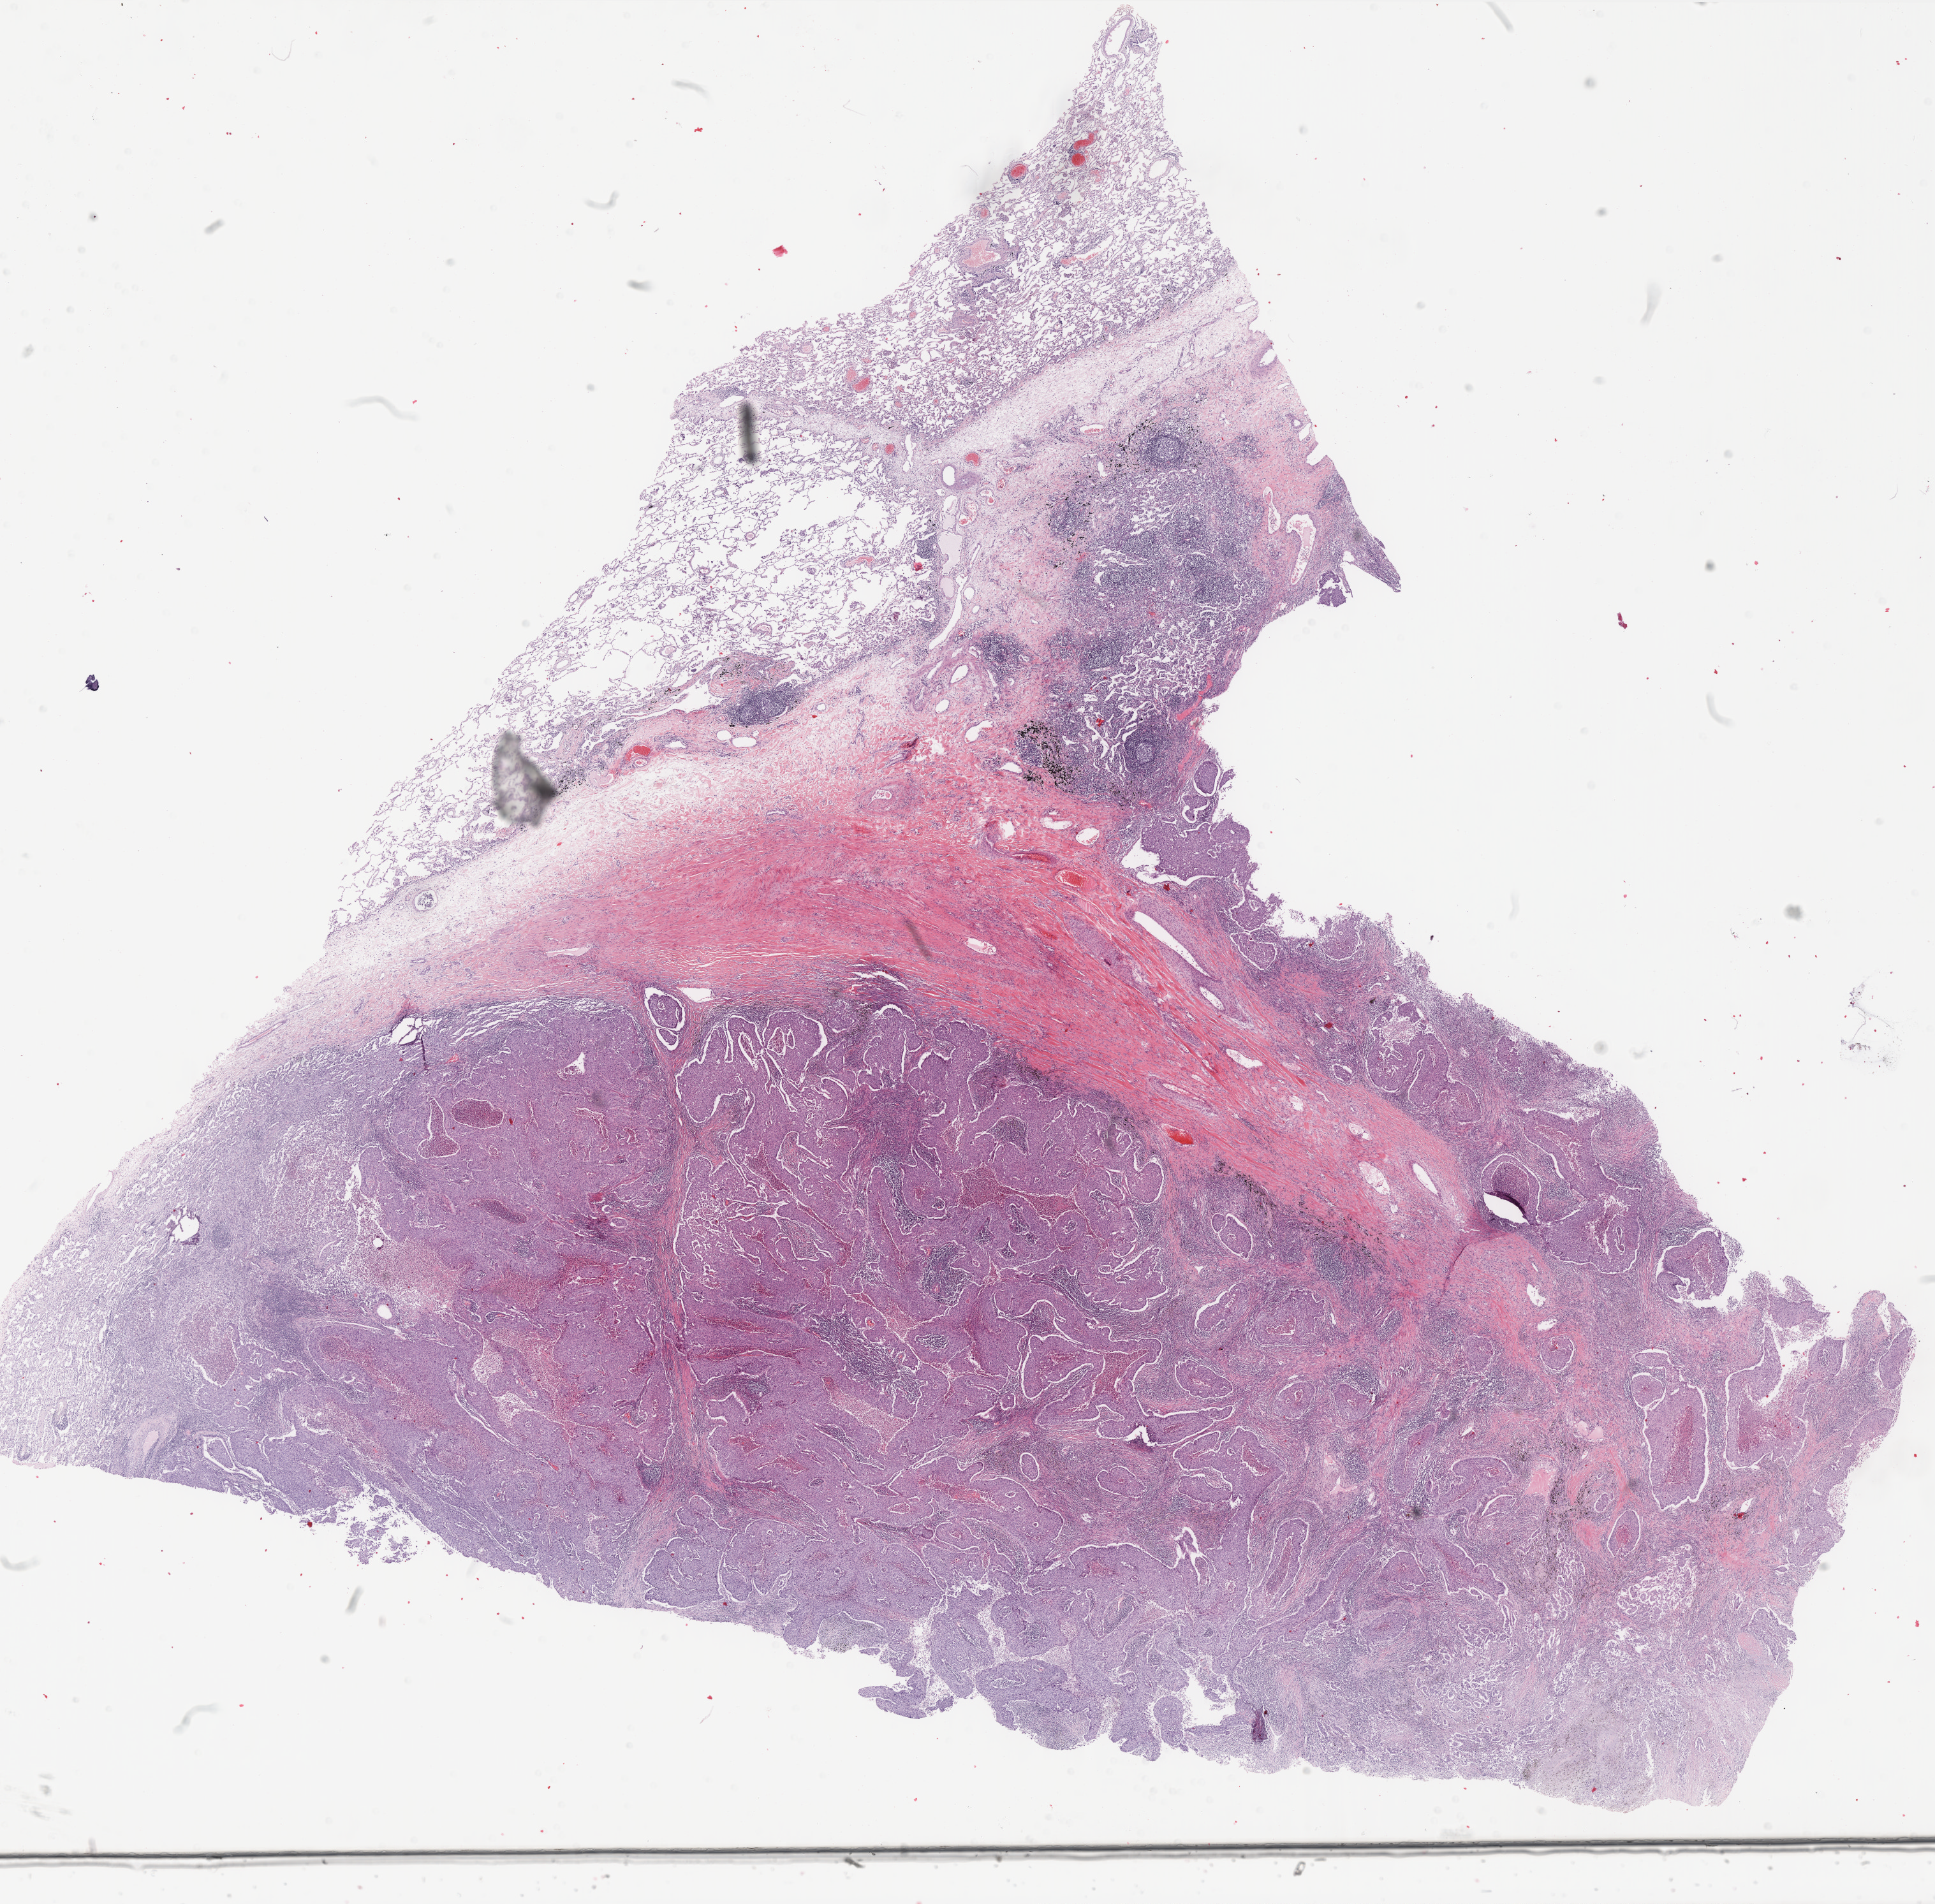
Whole-slide histology image, Hematoxylin and eosin (H&E) stained, a low-resolution overview of the entire scanned area, about 24.4 x 24.1 mm; FFPE section; sample: primary tumour, lung. Patient: male, age at initial diagnosis 64 years.
- diagnosis: Adenocarcinoma, NOS (upper lobe, lung)
- AJCC pathologic stage: IIB
- TNM: T2b N1 M0